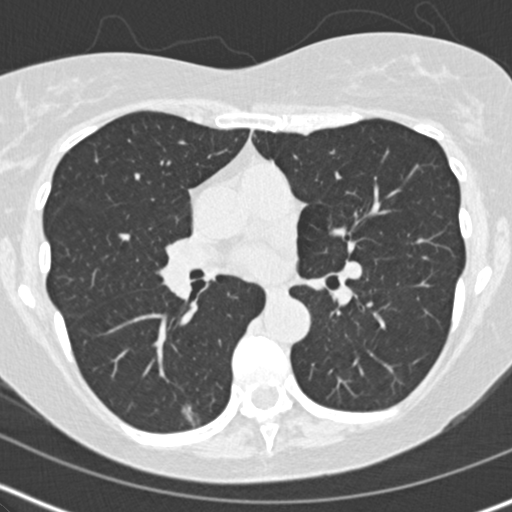
Axial slice from a low-dose chest CT screening exam. Second annual screen. Lung window (W 1500 / L -600 HU). 2 mm slice thickness. 512 × 512 image matrix, field of view 304 × 304 mm. Female participant, aged 60 years at enrolment. Former smoker at enrolment.
• Expert reader's lesion annotation, bounding box <167,389,221,436> (left, top, right, bottom; pixels).
• The screening reader recorded 2 non-calcified nodules or masses ≥4 mm on this exam (right middle lobe, right middle lobe); which of them this box marks is not recorded.